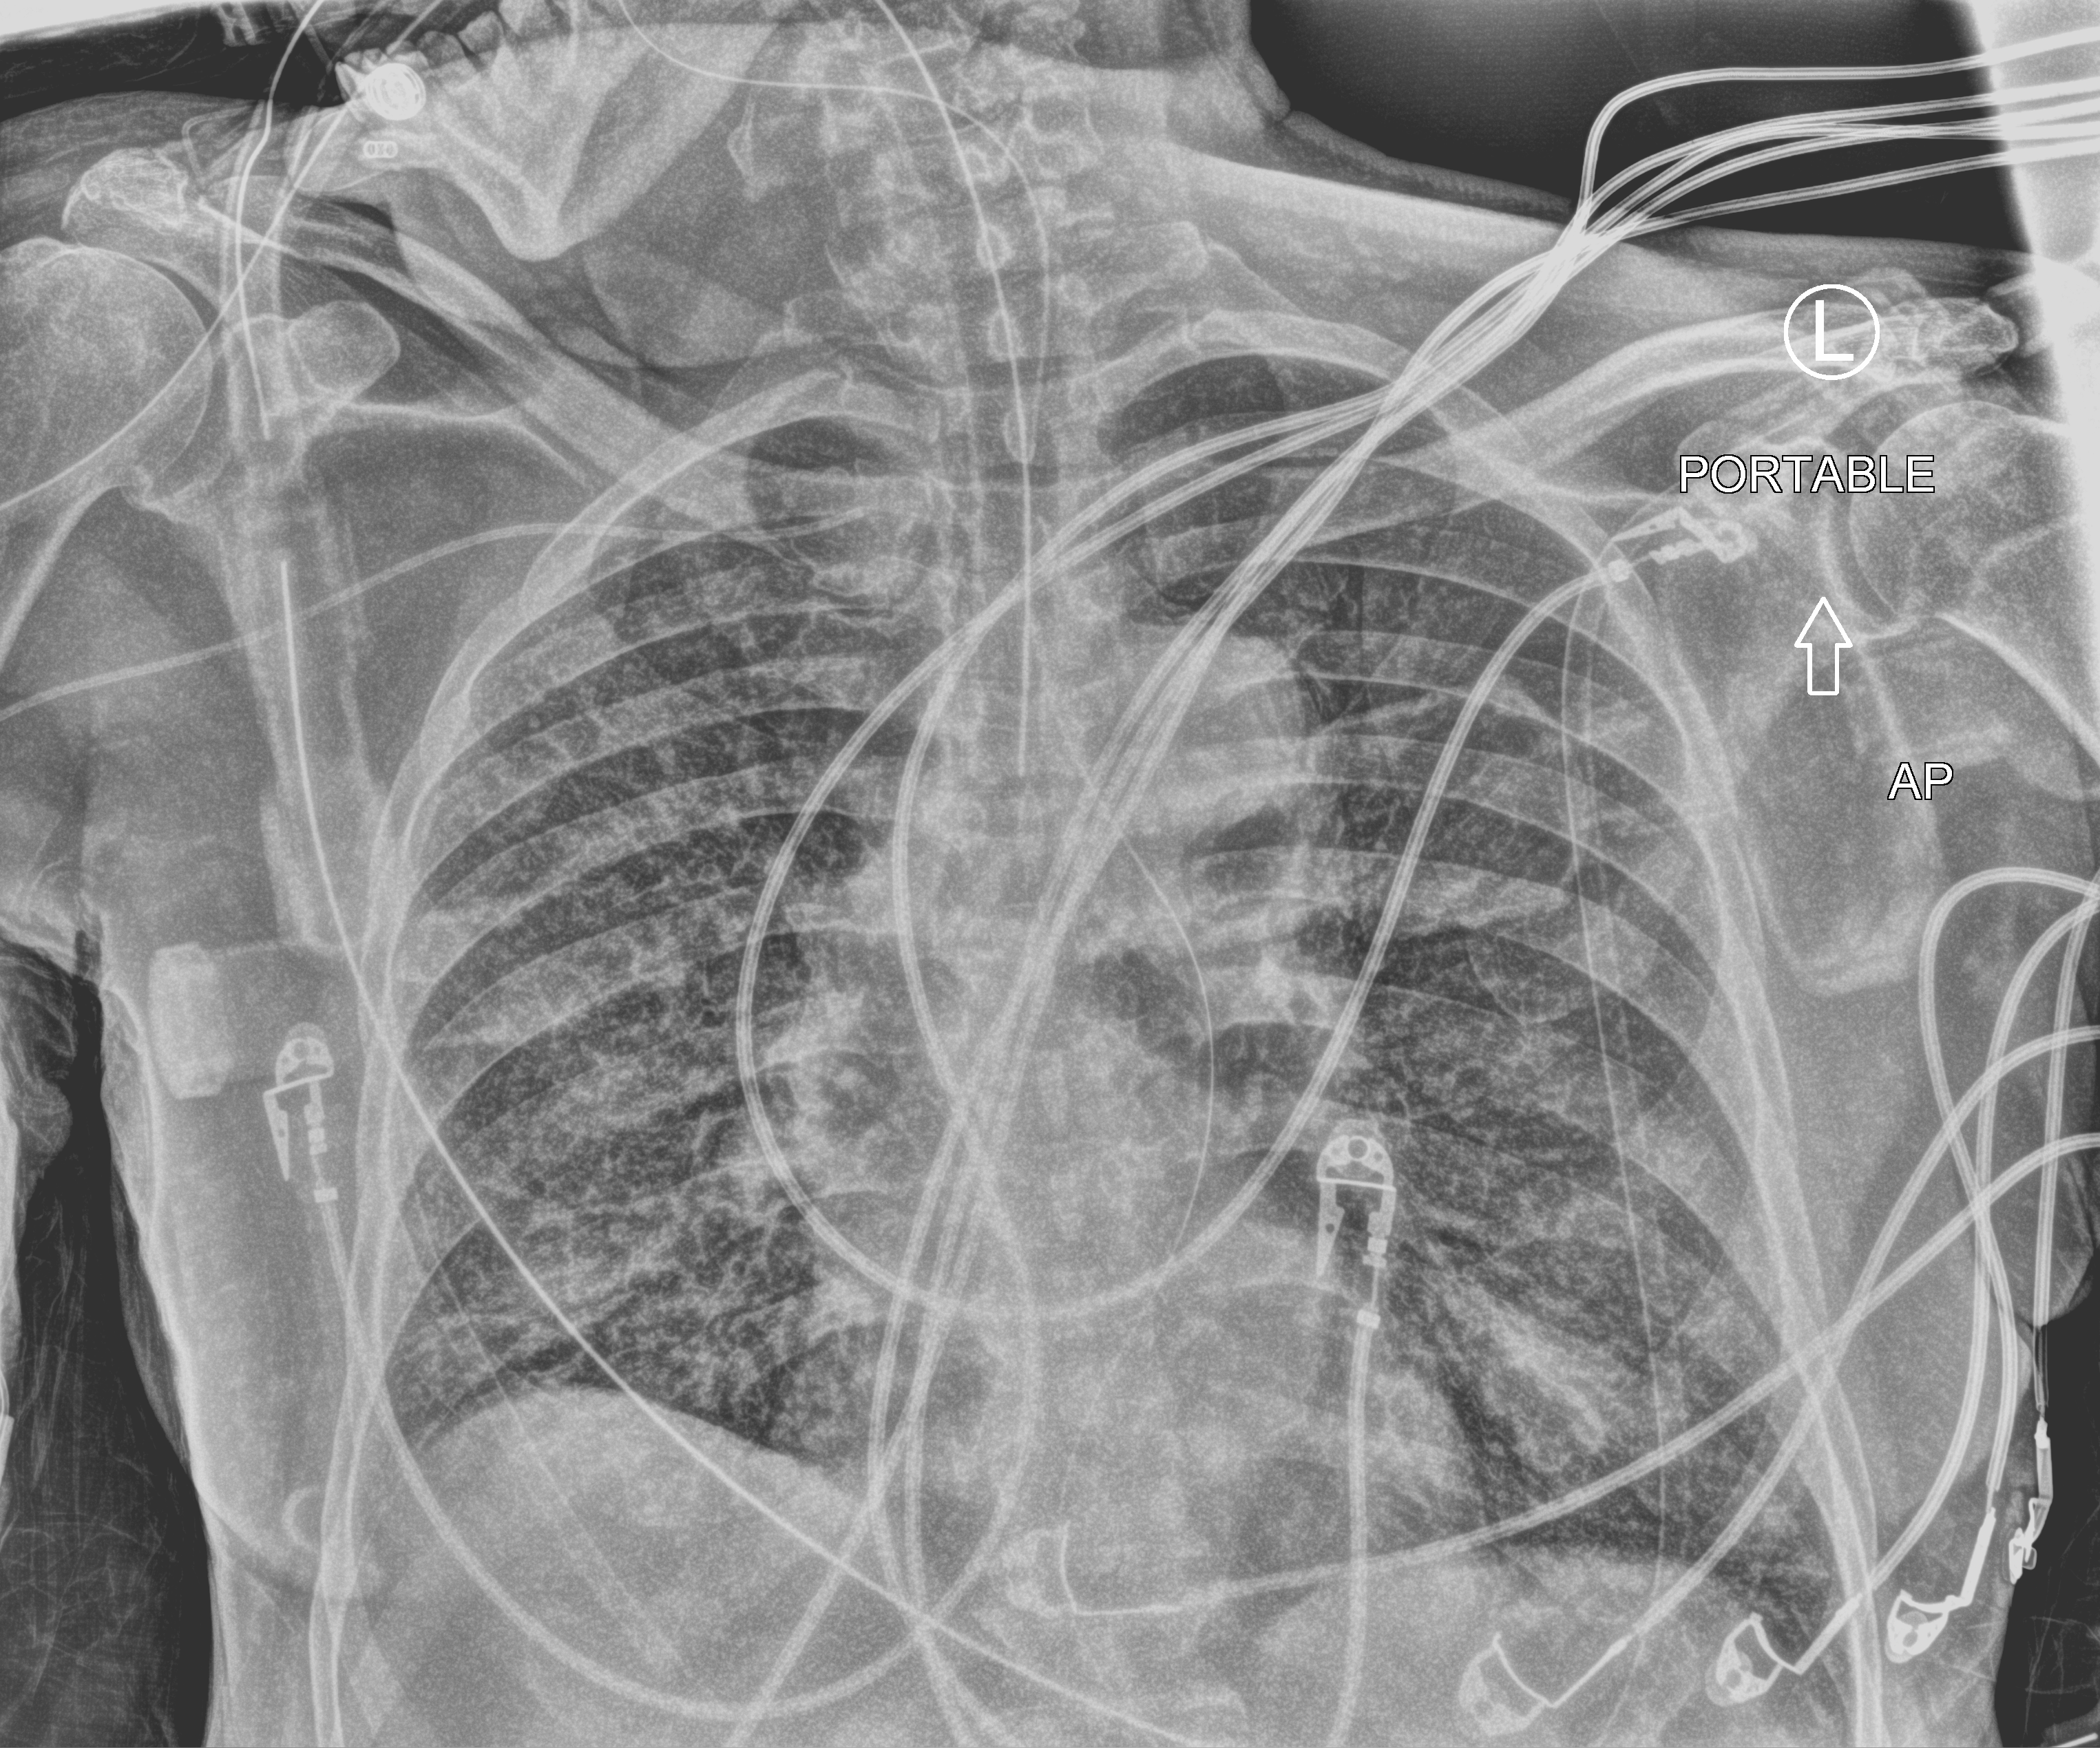
Chest X-ray (portable), anteroposterior (AP) projection. Patient hospitalised with COVID-19; male, aged 60–74 years.
Hospital-stay facts (about this admission, not read from this image; timing relative to this image not recorded):
- mechanically ventilated during this hospital stay: yes
- admitted to intensive care during this hospital stay: yes